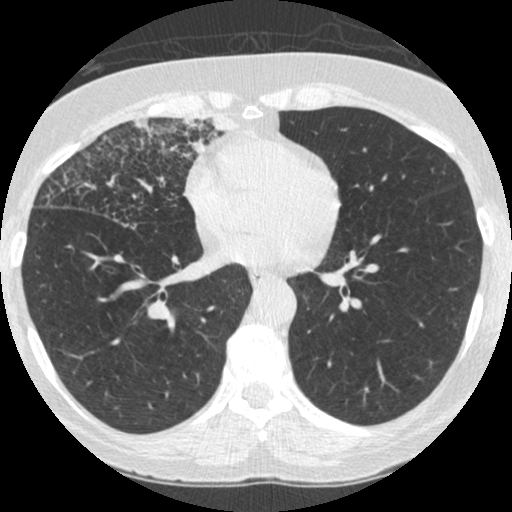
Low-dose screening chest CT, one axial slice; slice 117 of 253 in the series (ordered by position); reconstruction kernel STANDARD; 120 kVp; lung window (W 1500 / L -600 HU); 1.25 mm slice thickness; 512 × 512 image matrix, field of view 294 × 294 mm.
Outlined on this slice (outlined manually by an expert reader):
- lesion 4 (tumor, upper lobe of right lung): box from (x=182, y=115) to (x=234, y=153) px